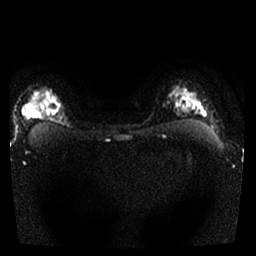
Breast MRI, one axial slice. Slice 23 of 25 in the series (ordered by position). Diffusion-weighted series; image 2 of 4 stored at this slice position (different b-values; order by instance number). 1.5 T. 4 mm slice thickness. 256 × 256 image matrix, field of view 300 × 300 mm. Female patient.
Annotated regions visible in this slice (manually delineated by an expert):
- tumour on diffusion-weighted imaging: bounding box (x1, y1, x2, y2) in pixels: (24, 96, 55, 116)